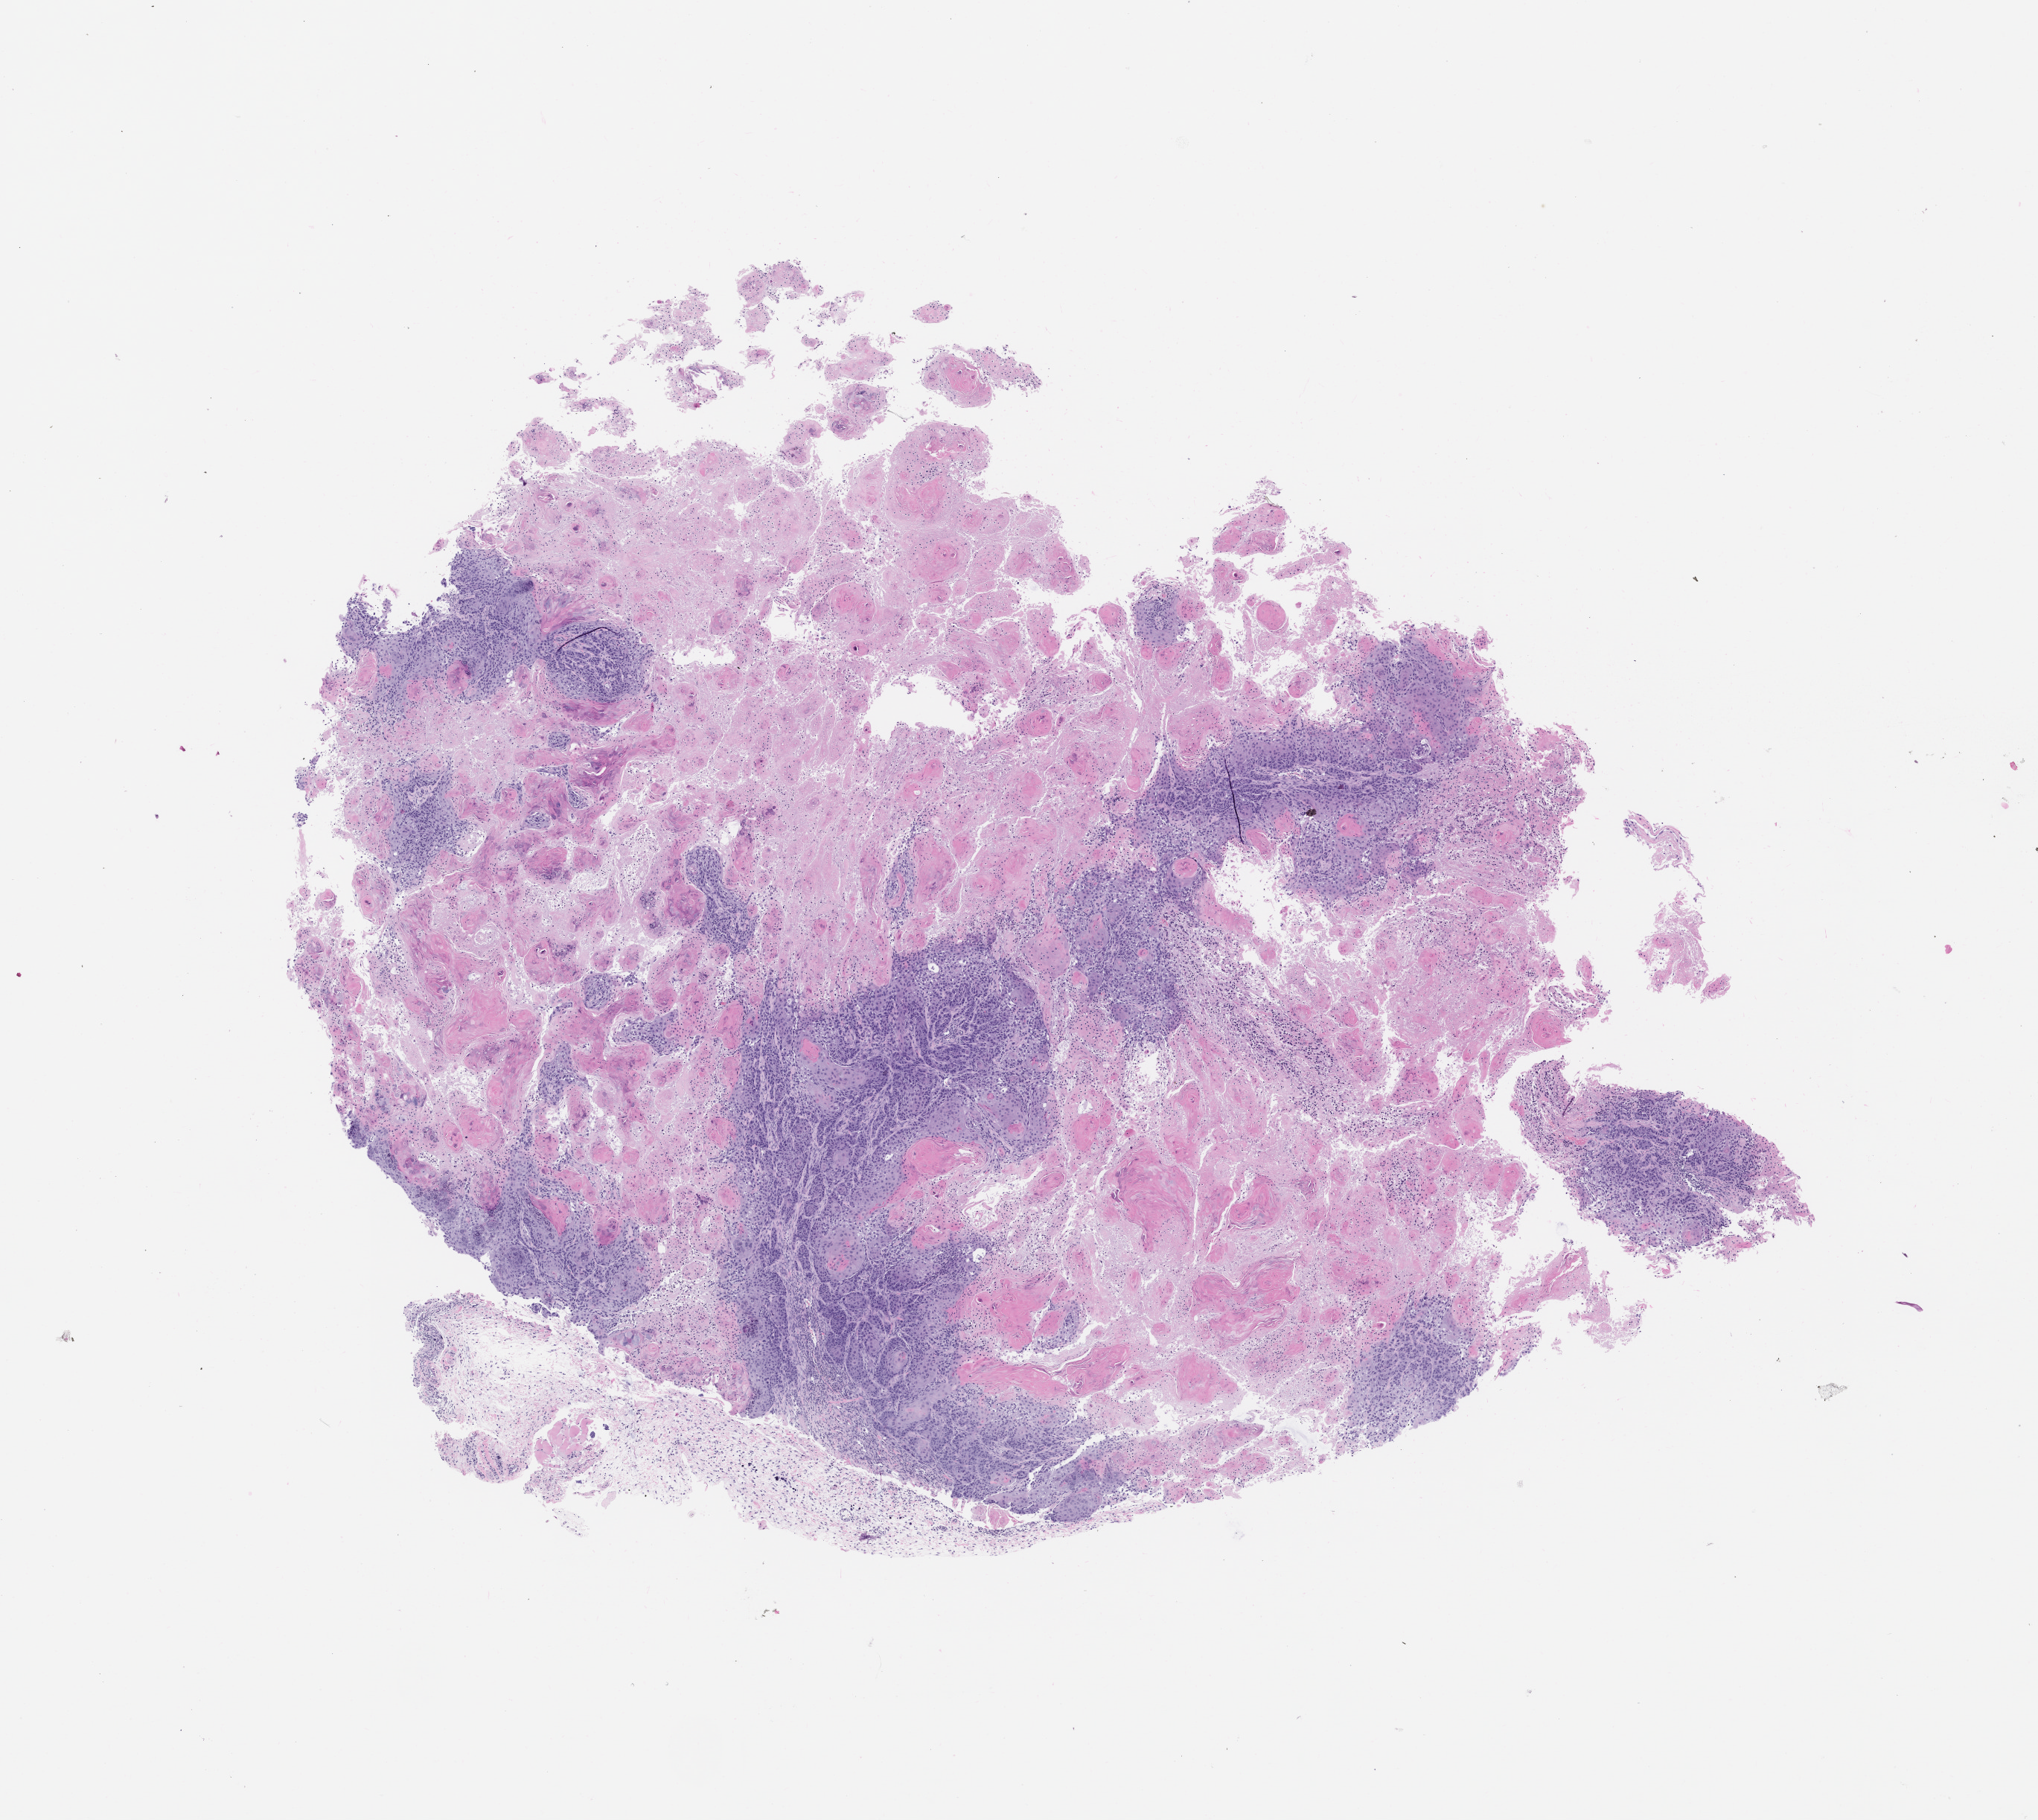
Whole-slide image, haematoxylin and eosin: patient-derived xenograft (human tumor grown in a mouse), passage 0, a low-resolution overview of the entire scanned area, about 11.0 x 9.8 mm; FFPE section; originating tumor site category: oral soft tissue.
• originating patient diagnosis: Head and Neck Squamous Cell Carcinoma